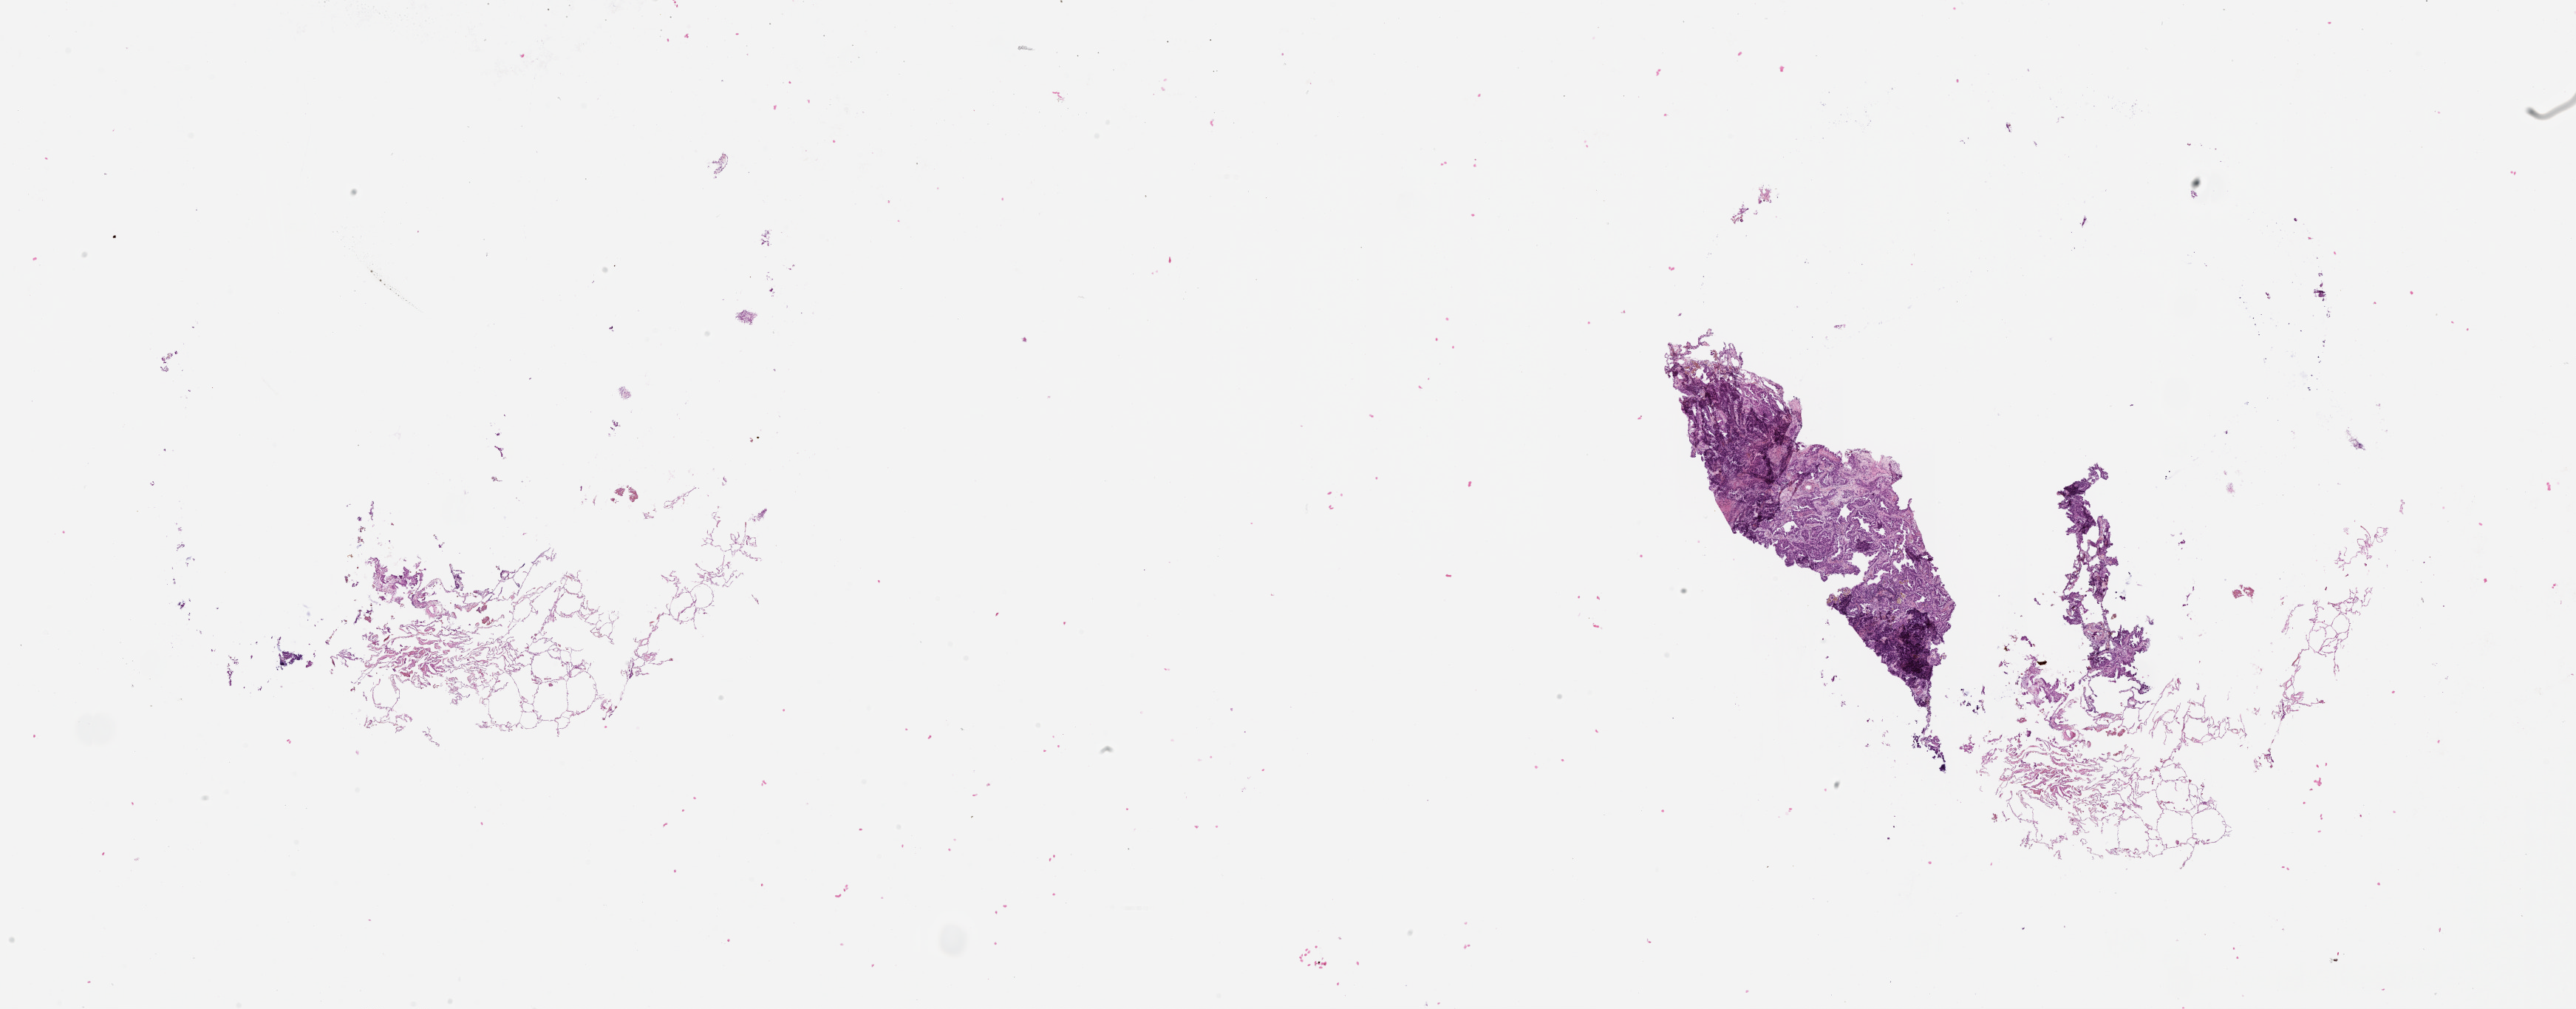
Digitized H&E tissue section (whole slide) — a low-resolution overview of the entire scanned area, about 28.1 x 11.0 mm, tumour tissue sample, sampled site: lung. Female, 63 y/o. Histologic grade: G2 (moderately differentiated). Pathologist review of this section (percent, as recorded): tumour nuclei 55%, necrosis 5%.
Primary tumour site (as recorded): right lower lobe. AJCC pathologic stage: IB. Histologic diagnosis: Adenocarcinoma, NOS.